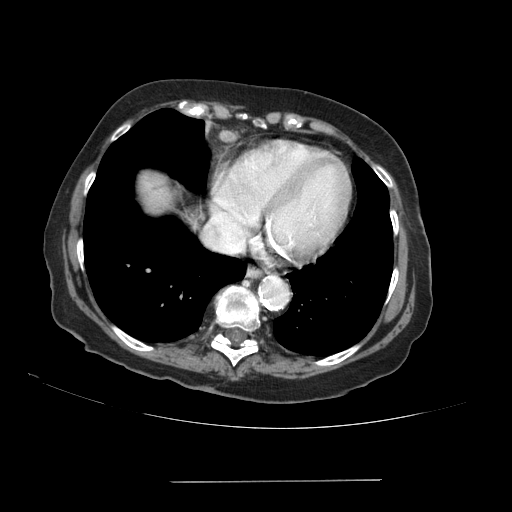
Contrast-enhanced abdominal CT (liver protocol), one axial slice. Slice 84 of 89 in the series (ordered by position). Reconstruction kernel STANDARD. 140 kVp. Soft-tissue window (W 400 / L 40 HU). 2.5 mm slice thickness. 512 × 512 image matrix. Case-level facts recorded for this patient, not image findings: diagnosis: hepatocellular carcinoma (patient treated with transarterial chemoembolisation; whether this scan precedes or follows treatment is not stated here); TNM stage (as recorded): Stage-IVA; Child-Pugh class: A; tumour differentiation: poorly differentiated; tumour nodularity: uninodular.
Outlined on this slice (semi-automatically segmented with operator editing):
- liver parenchyma outside the tumour (the mass and vessels are separate outlines, so this box may not span the whole liver): bounding box (x1, y1, x2, y2) in pixels: (138, 172, 172, 212)